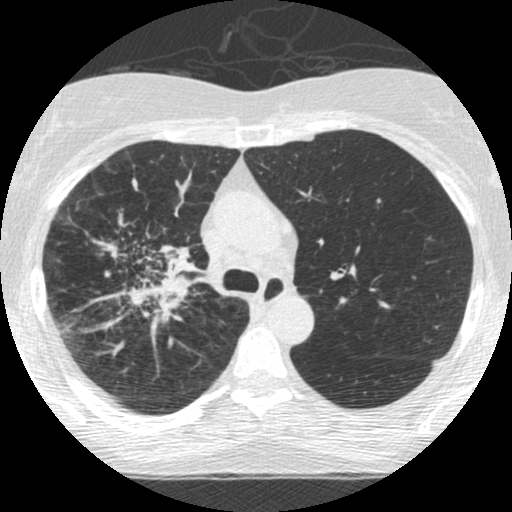
Low-dose screening chest CT, one axial slice. Position 179 of 253 along the scan axis. Reconstruction kernel STANDARD. Lung window (W 1500 / L -600 HU). 1.25 mm slice thickness. 512 × 512 image matrix.
Outlined on this slice (outlined manually by an expert reader):
- lesion 2 (tumor, hilum of right lung): box from (x=127, y=244) to (x=200, y=321) px